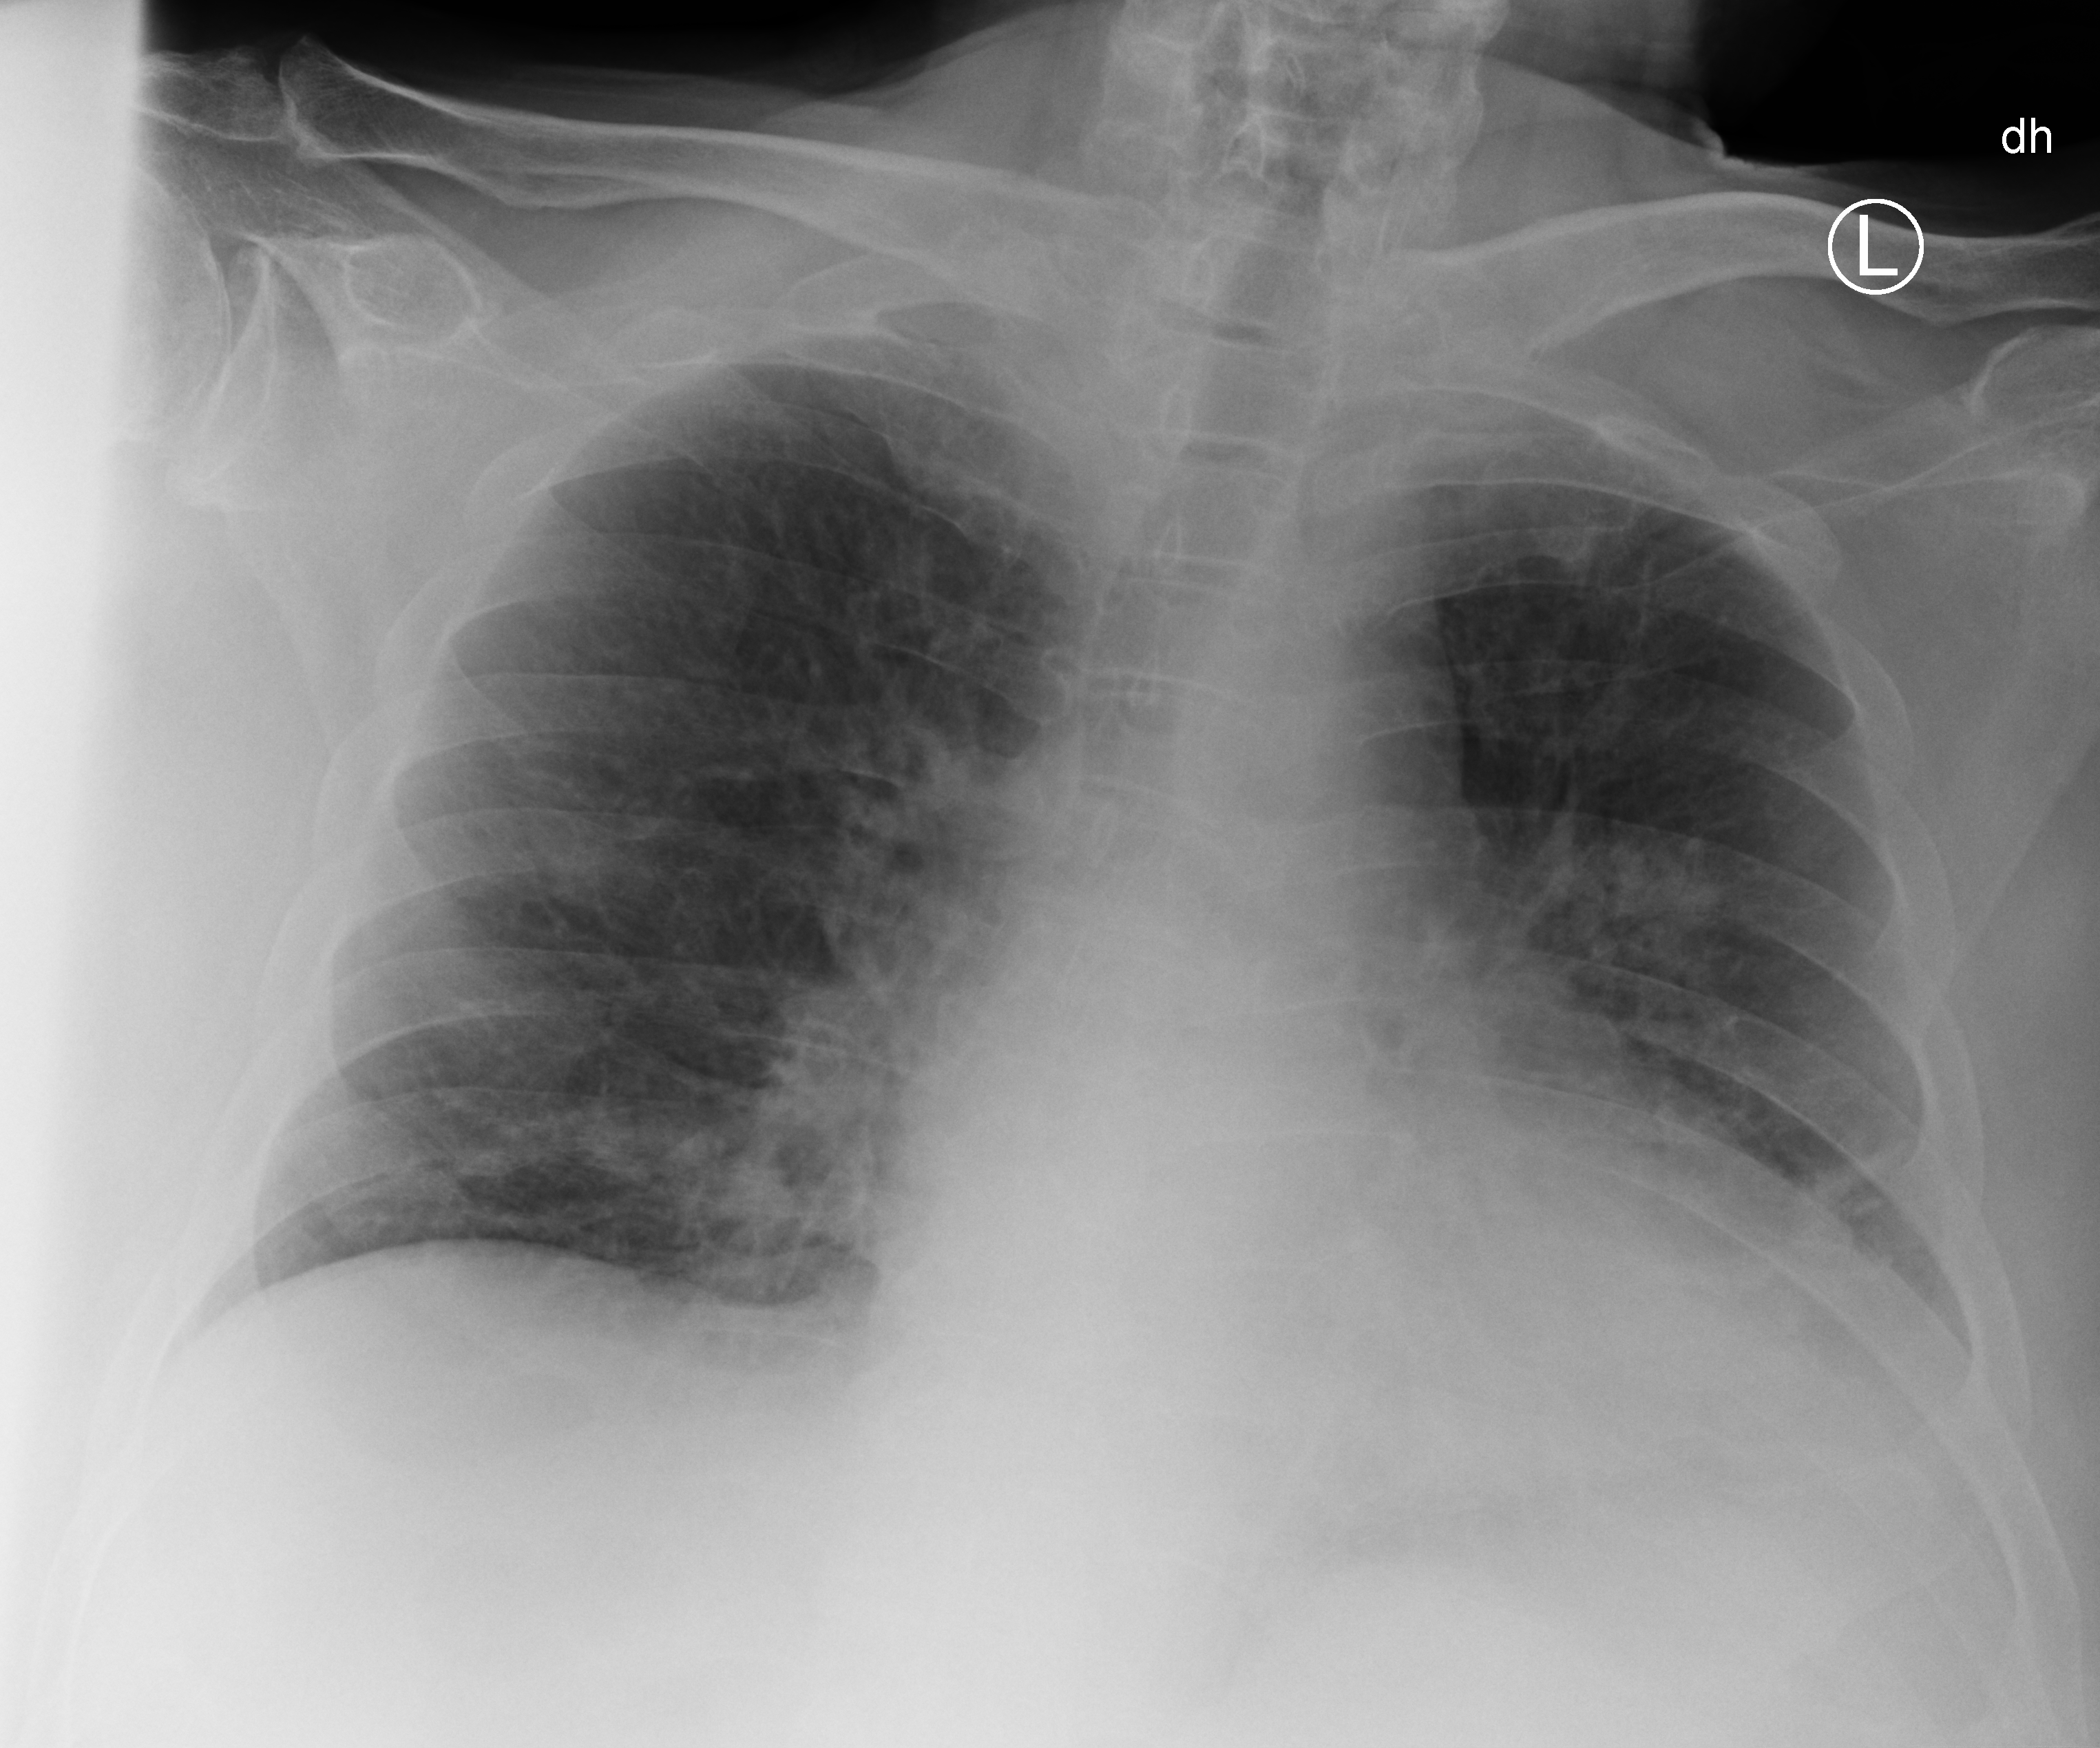
Bedside chest radiograph (computed radiography); anteroposterior (AP) projection. Patient hospitalised with COVID-19; male, aged 75–90 years.
From the hospital-stay record, not from the radiograph (when in the stay this image was taken is not recorded):
- mechanically ventilated during this hospital stay: no
- length of hospital stay: 1 day
- other chronic lung disease (admission record): no